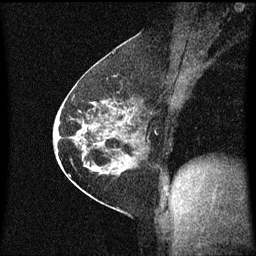
Breast MRI (dynamic contrast-enhanced), one sagittal slice; position 34 of 60 along the scan axis; dynamic contrast-enhanced series, image 2 of 3 at this slice position (ordered by acquisition); 1.5 T; TE 4.2 ms, TR 8.4 ms; 2 mm slice thickness; 256 × 256 image matrix. Patient: female, 60 years.
Annotated regions visible in this slice (semi-automatically segmented with operator editing):
- analysis volume of interest (the breast-tissue region the enhancement analysis was run in; not a lesion): bounding box (x1, y1, x2, y2) in pixels: (69, 66, 147, 193)
- tumour enhancement mask (voxels above the 70 % enhancement threshold inside the analysis volume of interest): (69, 72, 144, 171)